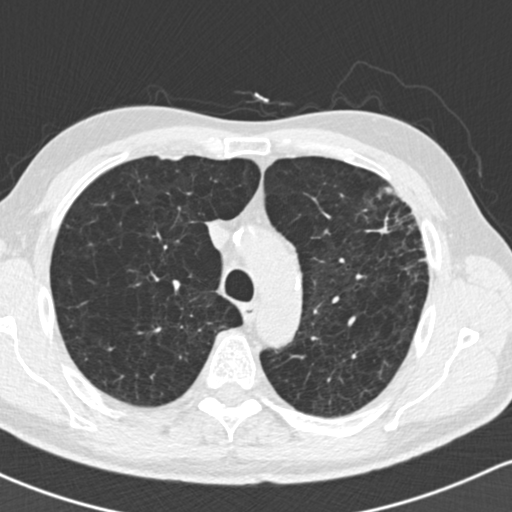
Axial slice from a low-dose chest CT screening exam; first (baseline) screen; lung window (W 1500 / L -600 HU); 2 mm slice thickness; slice 47 of 162 in the series; 512 × 512 image matrix, field of view 318 × 318 mm. Male, age 61 years at enrolment.
- Lesion marked by an expert reader, bounding box (x1, y1, x2, y2) in pixels: (351, 182, 442, 286).
- Screening reader's record for this exam (one nodule recorded; not confirmed to be the boxed lesion): non-calcified nodule or mass ≥4 mm, left upper lobe, 35 × 35 mm, spiculated (stellate) margins, soft tissue attenuation.
- Official screen result: positive, change unspecified: nodule(s) >= 4 mm or enlarging nodule(s), mass(es), or other non-specific abnormalities suspicious for lung cancer.